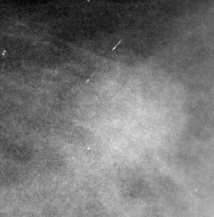
Region of interest cut from a scanned film mammogram (one marked finding); right breast; CC view.
- Marked abnormality: mass, shape oval, margins ill defined; BI-RADS assessment category 4; pathology (as recorded): malignant.